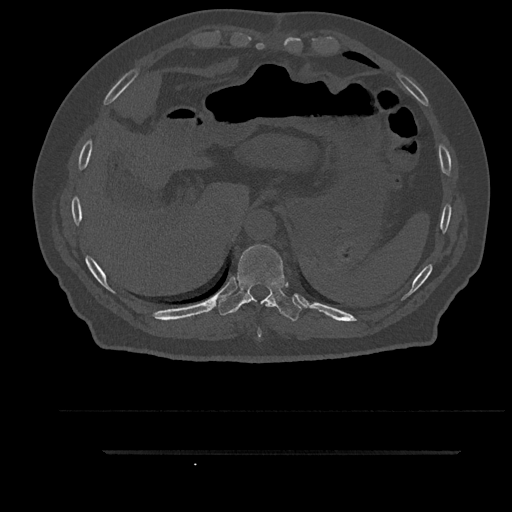
CT including the spine, one axial slice; slice 380 of 797 in the series (ordered by position); reconstruction kernel Br40s/3; 120 kVp; bone window (W 1800 / L 400 HU); 512 × 512 image matrix, field of view 432 × 432 mm. Patient: male, 63 years. From the clinical record (not read from this slice): primary cancer: renal; vertebrae with lytic lesions (as recorded): T8.
Annotated regions visible in this slice (semi-automatic segmentation, software-assisted and operator-edited):
- T10 vertebra: bounding box (x1, y1, x2, y2) in pixels: (218, 245, 303, 321)
- T9 vertebra: (258, 302, 269, 337)